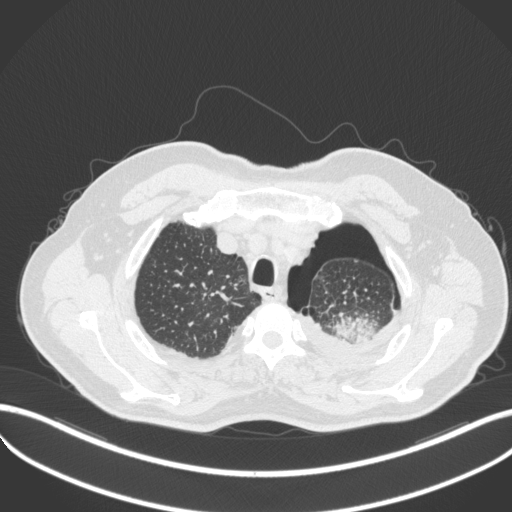
Chest CT, one axial slice; position 420 of 466 along the scan axis; 120 kVp; lung window (W 1500 / L -600 HU); 1 mm slice thickness; 512 × 512 image matrix, field of view 400 × 400 mm. Patient: male, 76 years. From the clinical record (not read from this slice): clinical TNM (as recorded): T3 N0 M1b.
Annotated regions visible in this slice (bounding box drawn by a radiologist):
- lung tumour (recorded histology: adenocarcinoma): box from (x=333, y=310) to (x=380, y=346) px